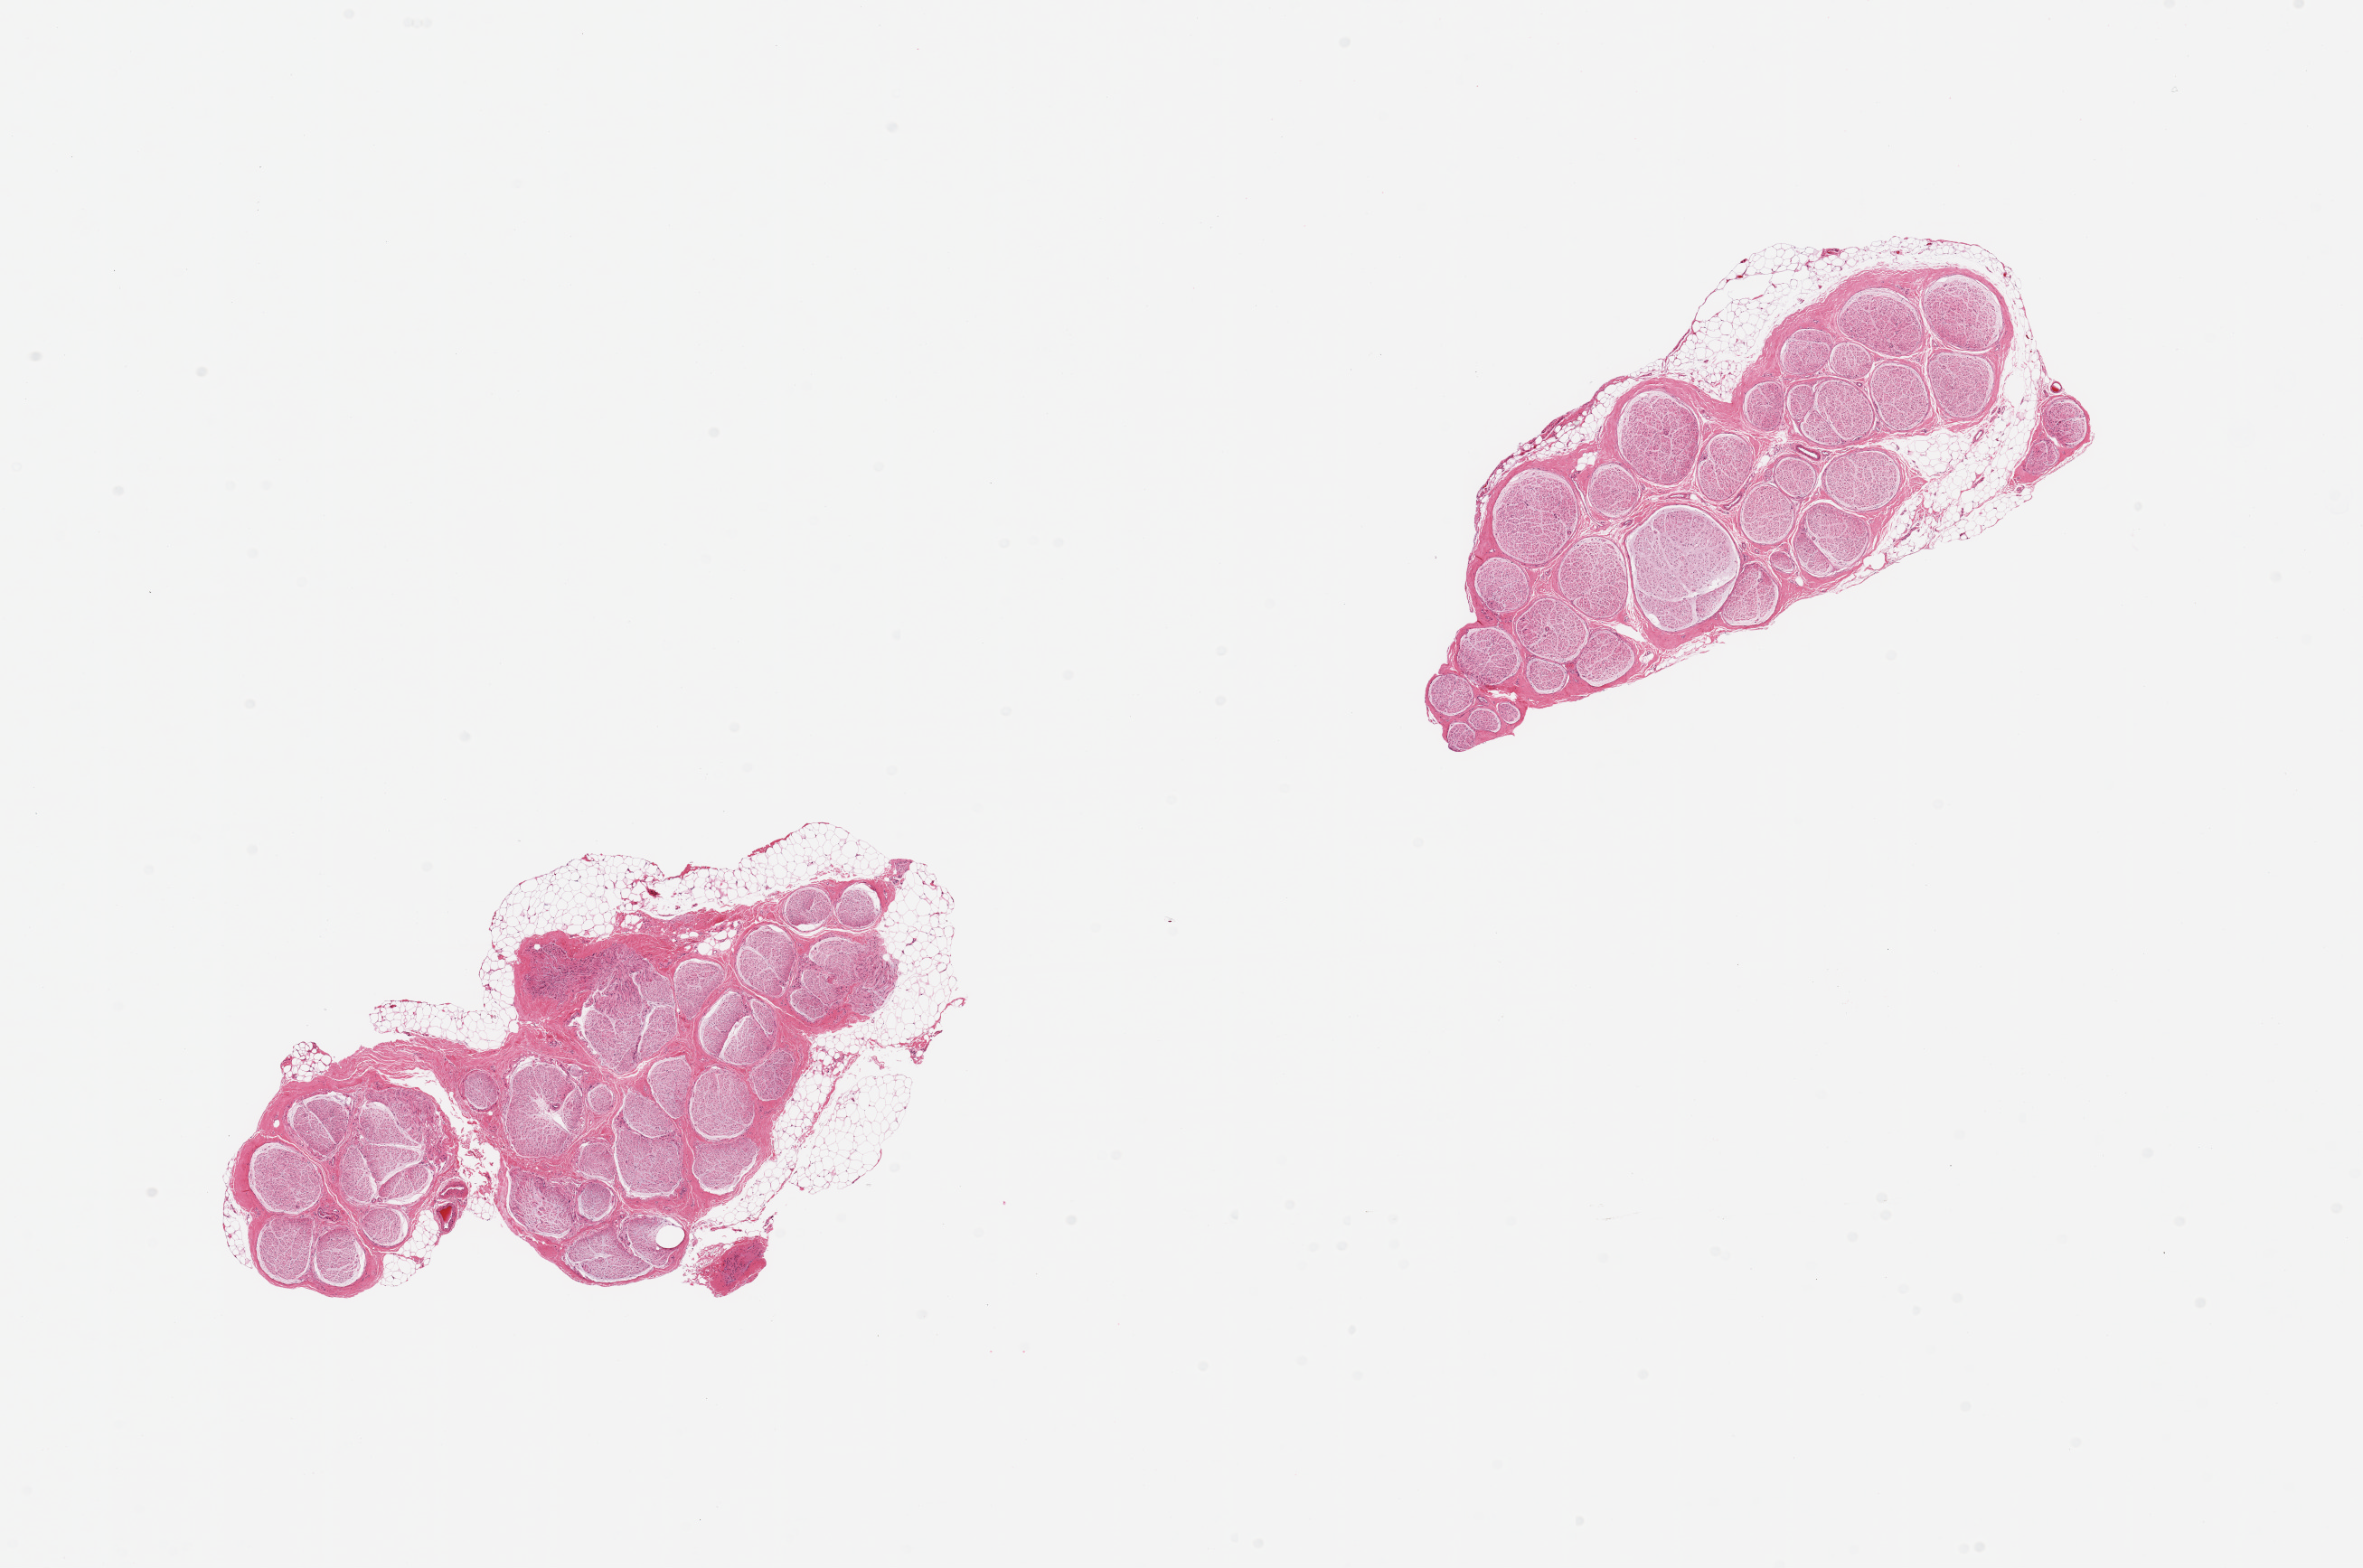
Digitized hematoxylin and eosin (H&E)-stained section, a low-resolution overview of the entire scanned area, about 20.7 x 13.7 mm (from a 20x scan), PAXgene-fixed paraffin-embedded (PFPE) section, sampled site (target tissue): tibial nerve, donor tissue sample. Donor sex: female.
• review note (as recorded): 2 pieces; 20% external fat